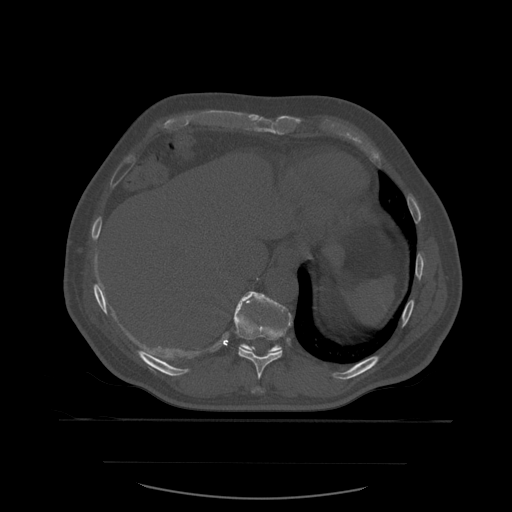
CT including the spine, one axial slice. Bone window (W 1800 / L 400 HU). 1.25 mm slice thickness. 512 × 512 image matrix, field of view 479 × 479 mm. Patient age 71 years. From the clinical record (not read from this slice): primary cancer: lung; vertebrae with lytic lesions (as recorded): T1, T2, L5, S1.
Structures marked on this image (semi-automatically segmented with operator editing):
- T10 vertebra: bounding box [x1, y1, x2, y2] px = [234, 292, 293, 380]
- T11 vertebra: [237, 292, 293, 353]
- T9 vertebra: [252, 387, 264, 393]